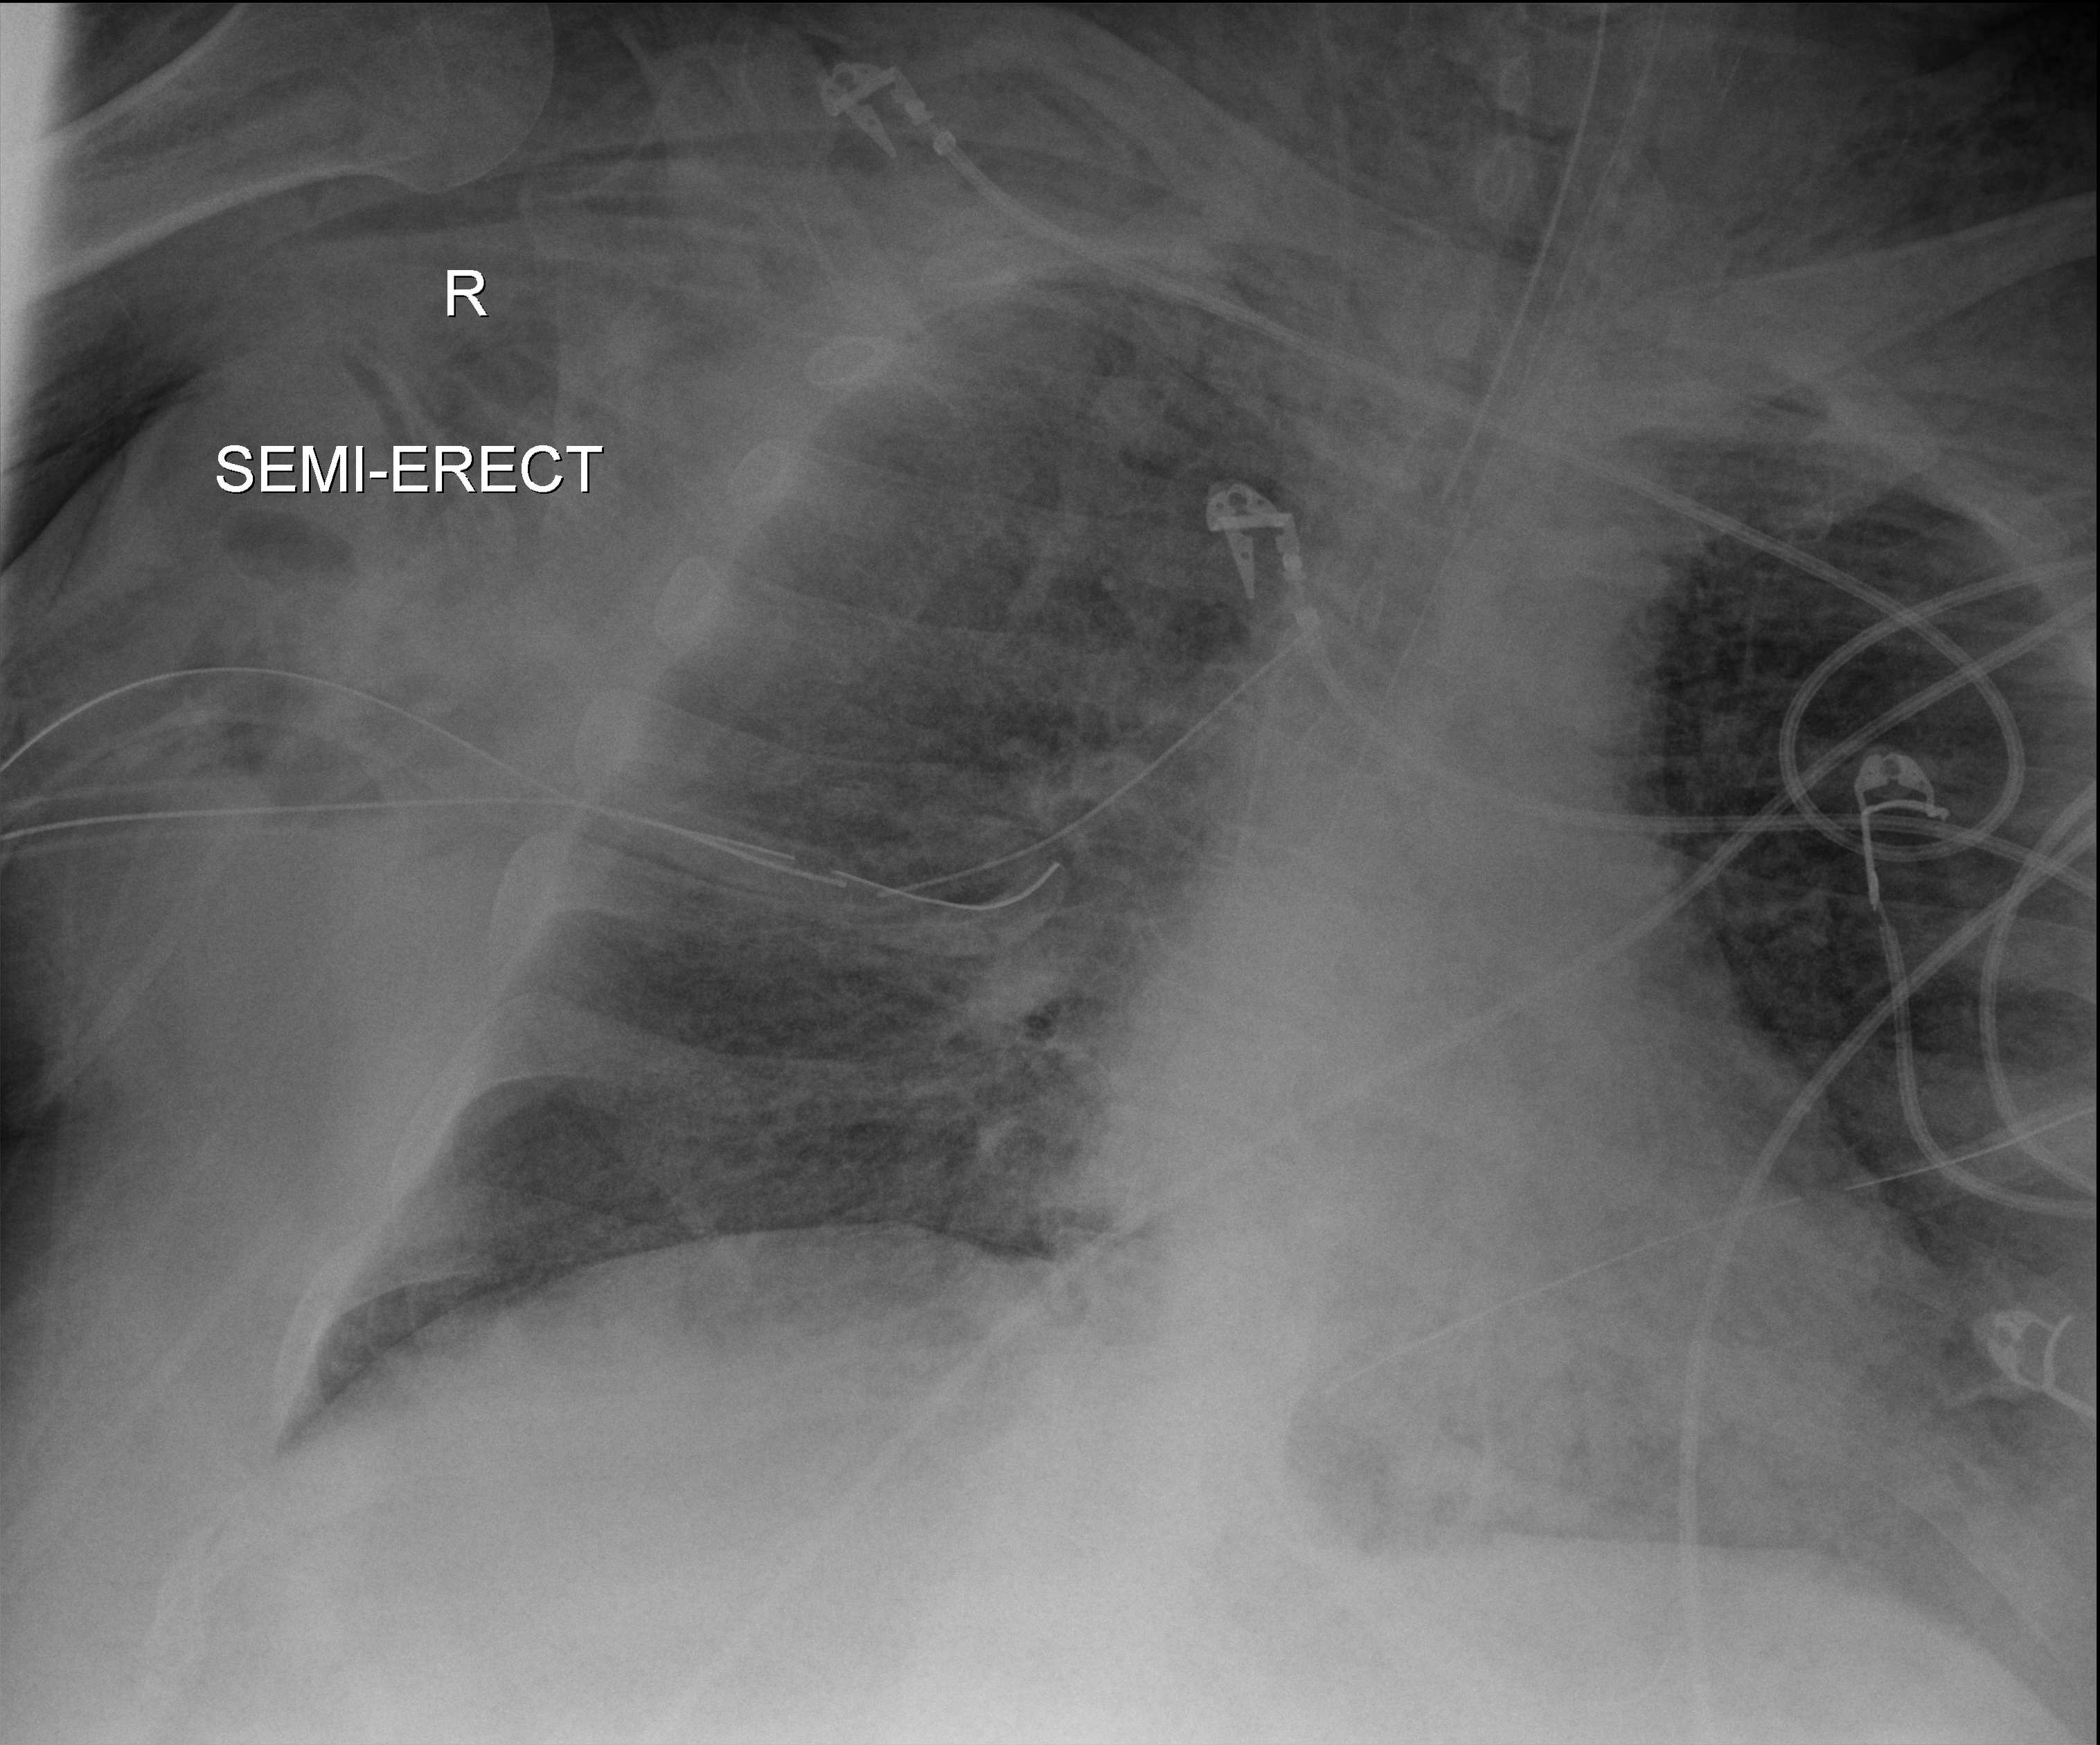
Portable chest radiograph, anteroposterior (AP) projection. Patient hospitalised with COVID-19, aged 18–59 years.
Hospital-stay facts (about this admission, not read from this image; timing relative to this image not recorded): admitted to intensive care during this hospital stay: yes; diabetes (admission record): yes.